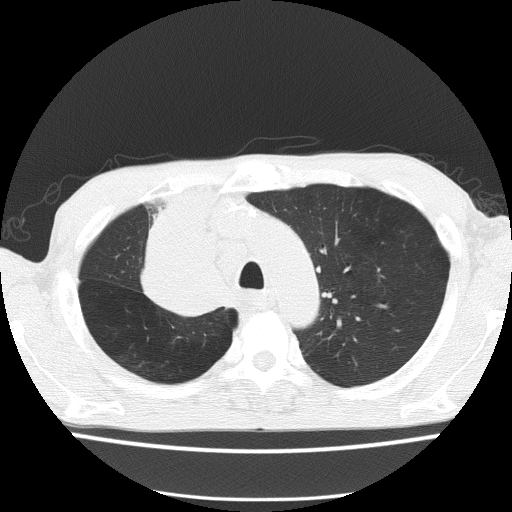
Low-dose screening chest CT, one axial slice. Position 114 of 150 along the scan axis. Lung window (W 1500 / L -600 HU). 2 mm slice thickness. 512 × 512 image matrix, field of view 336 × 336 mm.
Outlined on this slice (expert manual segmentation):
- lesion 1 (tumor, hilum of right lung): bounding box [x1, y1, x2, y2] px = [144, 187, 220, 315]